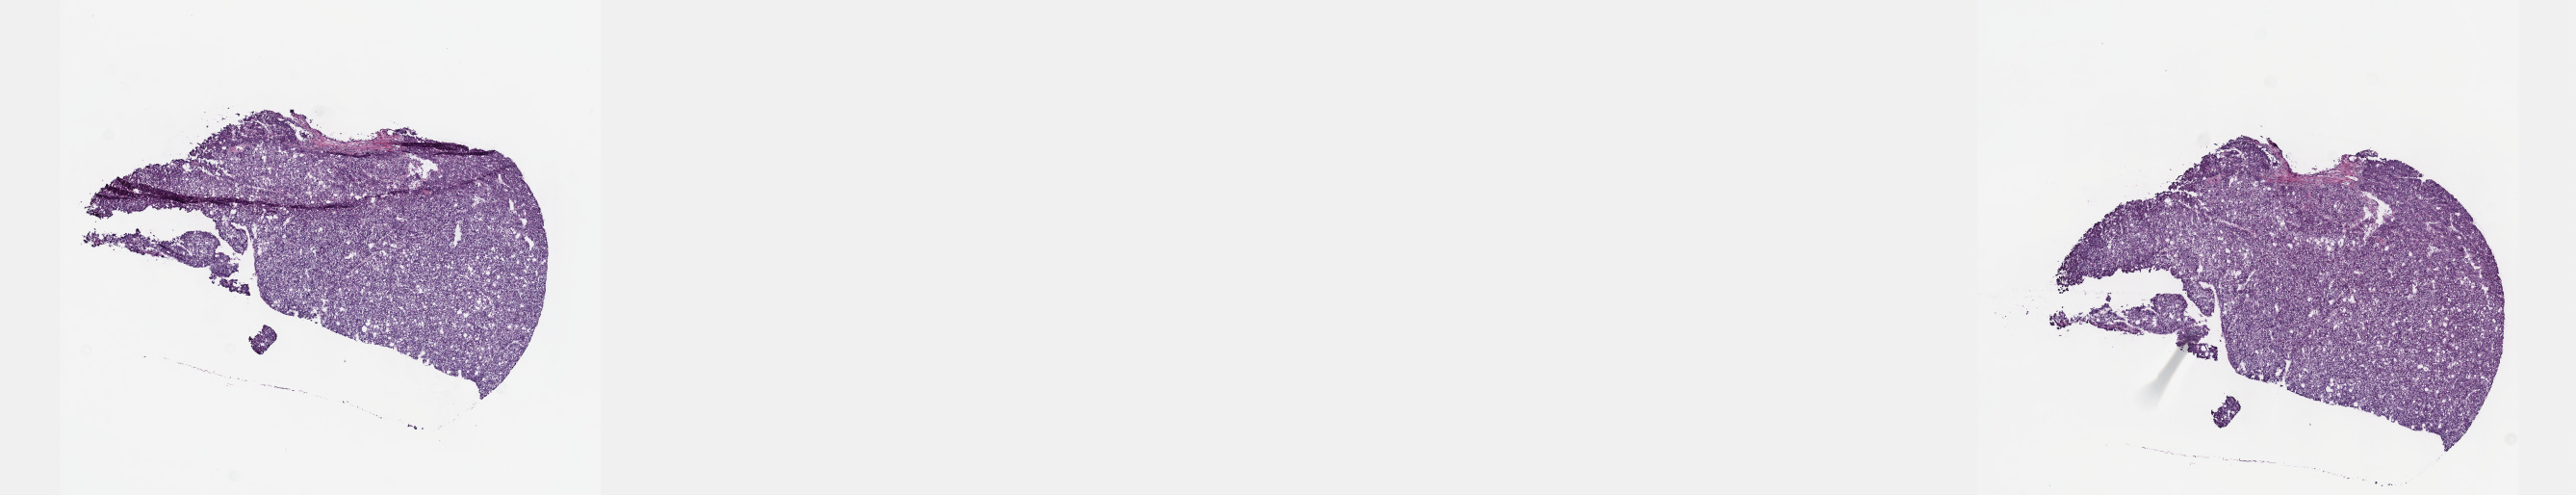
Whole-slide histology image, H&E-stained — a low-resolution overview of the entire scanned area, about 21.6 x 4.2 mm, frozen section, sample: primary tumour, liver. Male, age 65 years at initial diagnosis. Composition of this section per pathologist review: tumour cells 95%, tumour nuclei 96%.
Diagnosis: Hepatocellular carcinoma, NOS.